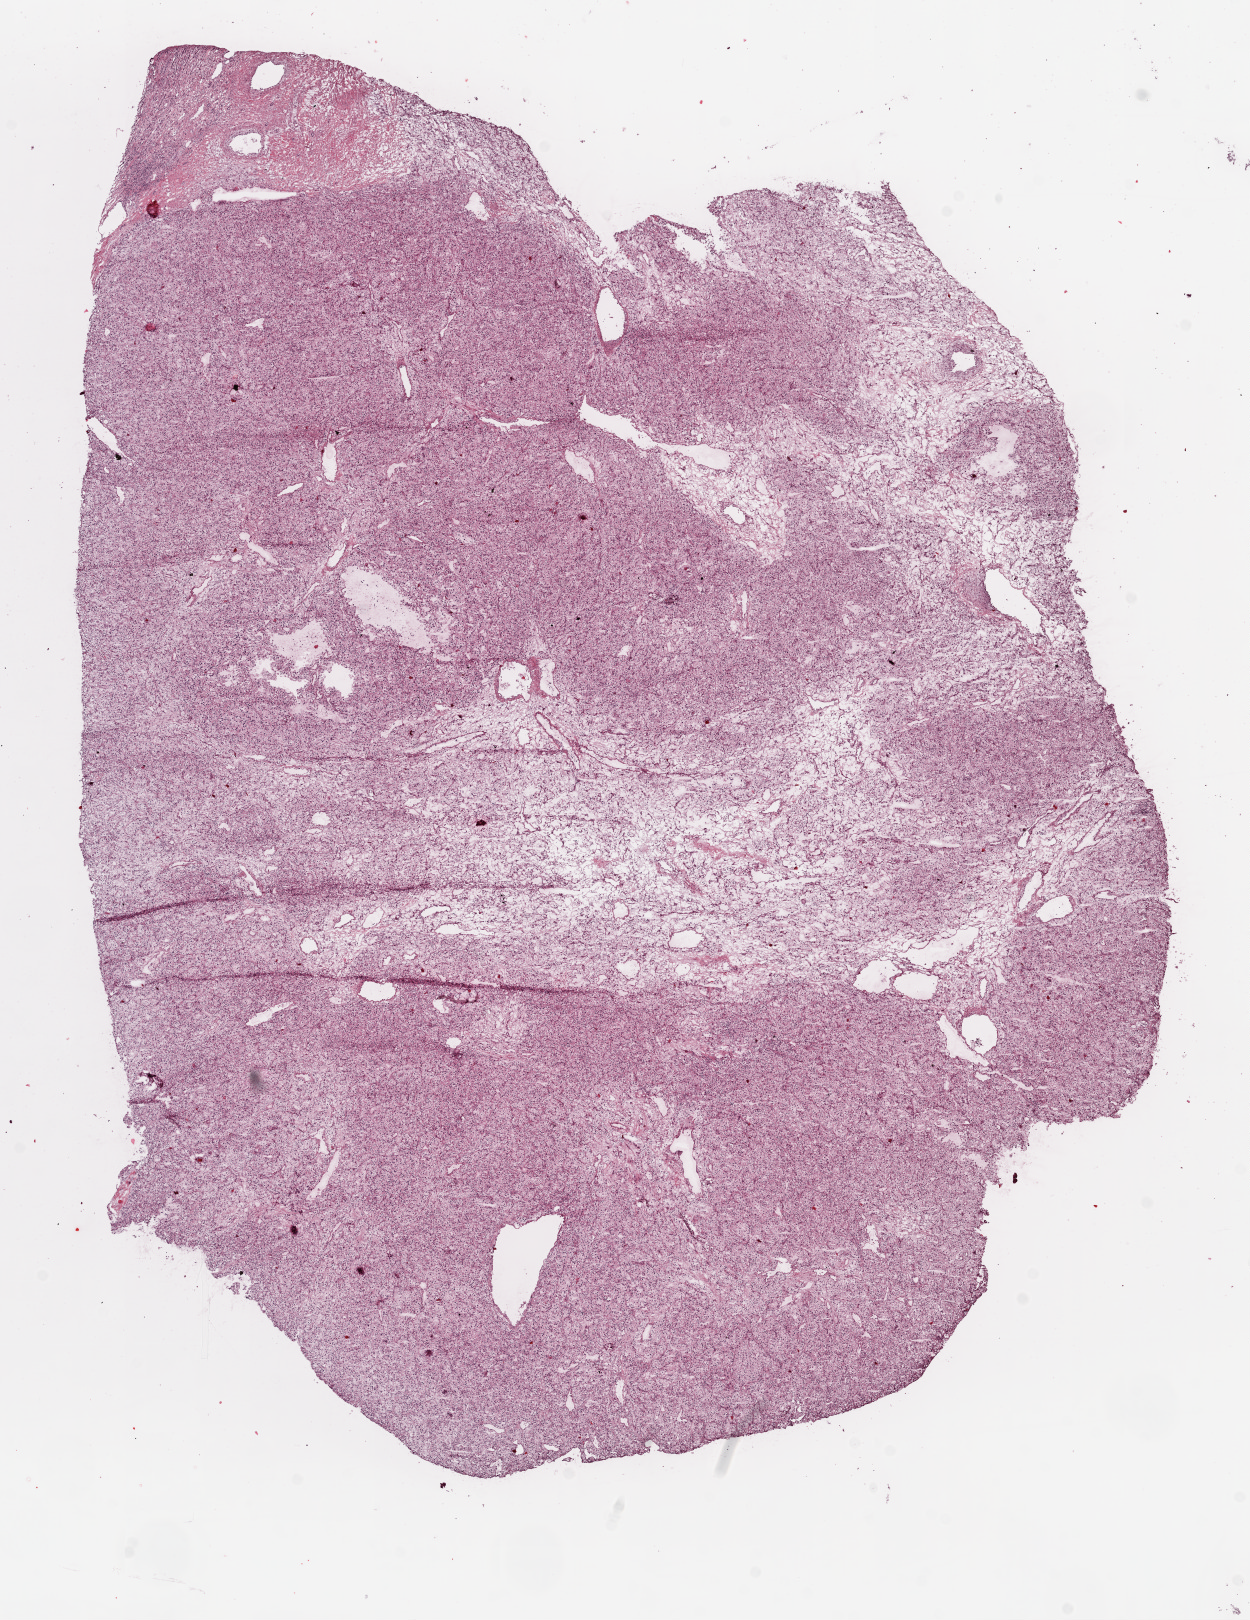
Digitized H&E-stained tissue section (whole slide) — shown as a low-resolution overview of the whole scanned area (about 10.0 x 13.0 mm), frozen section from the top of the tissue portion, primary tumour sample from the kidney. Male, age 50 years at initial diagnosis. Histologic grade: G2 (moderately differentiated). Pathologist review of this section (percent, as recorded): tumour cells 97%, tumour nuclei 80%, stromal cells 3%, necrosis 0%. Infiltration values recorded for this section: lymphocyte infiltration 2%.
- laterality: left
- pathologic diagnosis: Clear cell adenocarcinoma, NOS
- AJCC pathologic stage: I